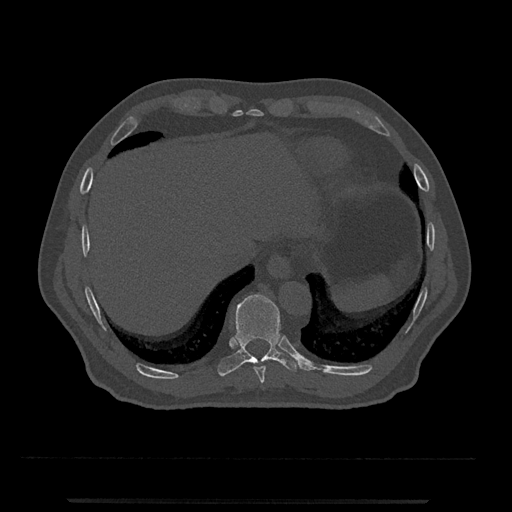
CT including the spine, one axial slice. Position 534 of 797 along the scan axis. 120 kVp. Bone window (W 1800 / L 400 HU). 0.5 mm slice thickness. 512 × 512 image matrix, field of view 419 × 419 mm. Patient: male, 63 years. From the clinical record (not read from this slice): primary cancer: prostate.
Annotated regions visible in this slice (semi-automatically segmented with operator editing):
- T10 vertebra: bounding box (x1, y1, x2, y2) in pixels: (218, 294, 300, 377)
- T9 vertebra: (254, 366, 266, 383)